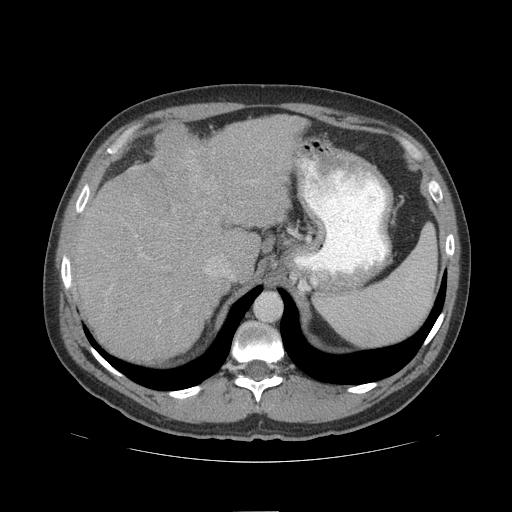
Contrast-enhanced abdominal CT (liver protocol), one axial slice. Position 75 of 109 along the scan axis. Soft-tissue window (W 400 / L 40 HU). 2.5 mm slice thickness. 512 × 512 image matrix, field of view 420 × 420 mm. Case-level facts recorded for this patient, not image findings: diagnosis: hepatocellular carcinoma (patient treated with transarterial chemoembolisation; whether this scan precedes or follows treatment is not stated here); TNM stage (as recorded): Stage-IIIB; Child-Pugh class: A; tumour differentiation: poorly differentiated; tumour nodularity: multinodular.
Outlined on this slice (semi-automatically segmented with operator editing):
- liver parenchyma outside the tumour (the mass and vessels are separate outlines, so this box may not span the whole liver): bounding box <72,114,305,362> (left, top, right, bottom; pixels)
- mass: <146,122,232,215>
- liver vessels: <207,269,209,271>